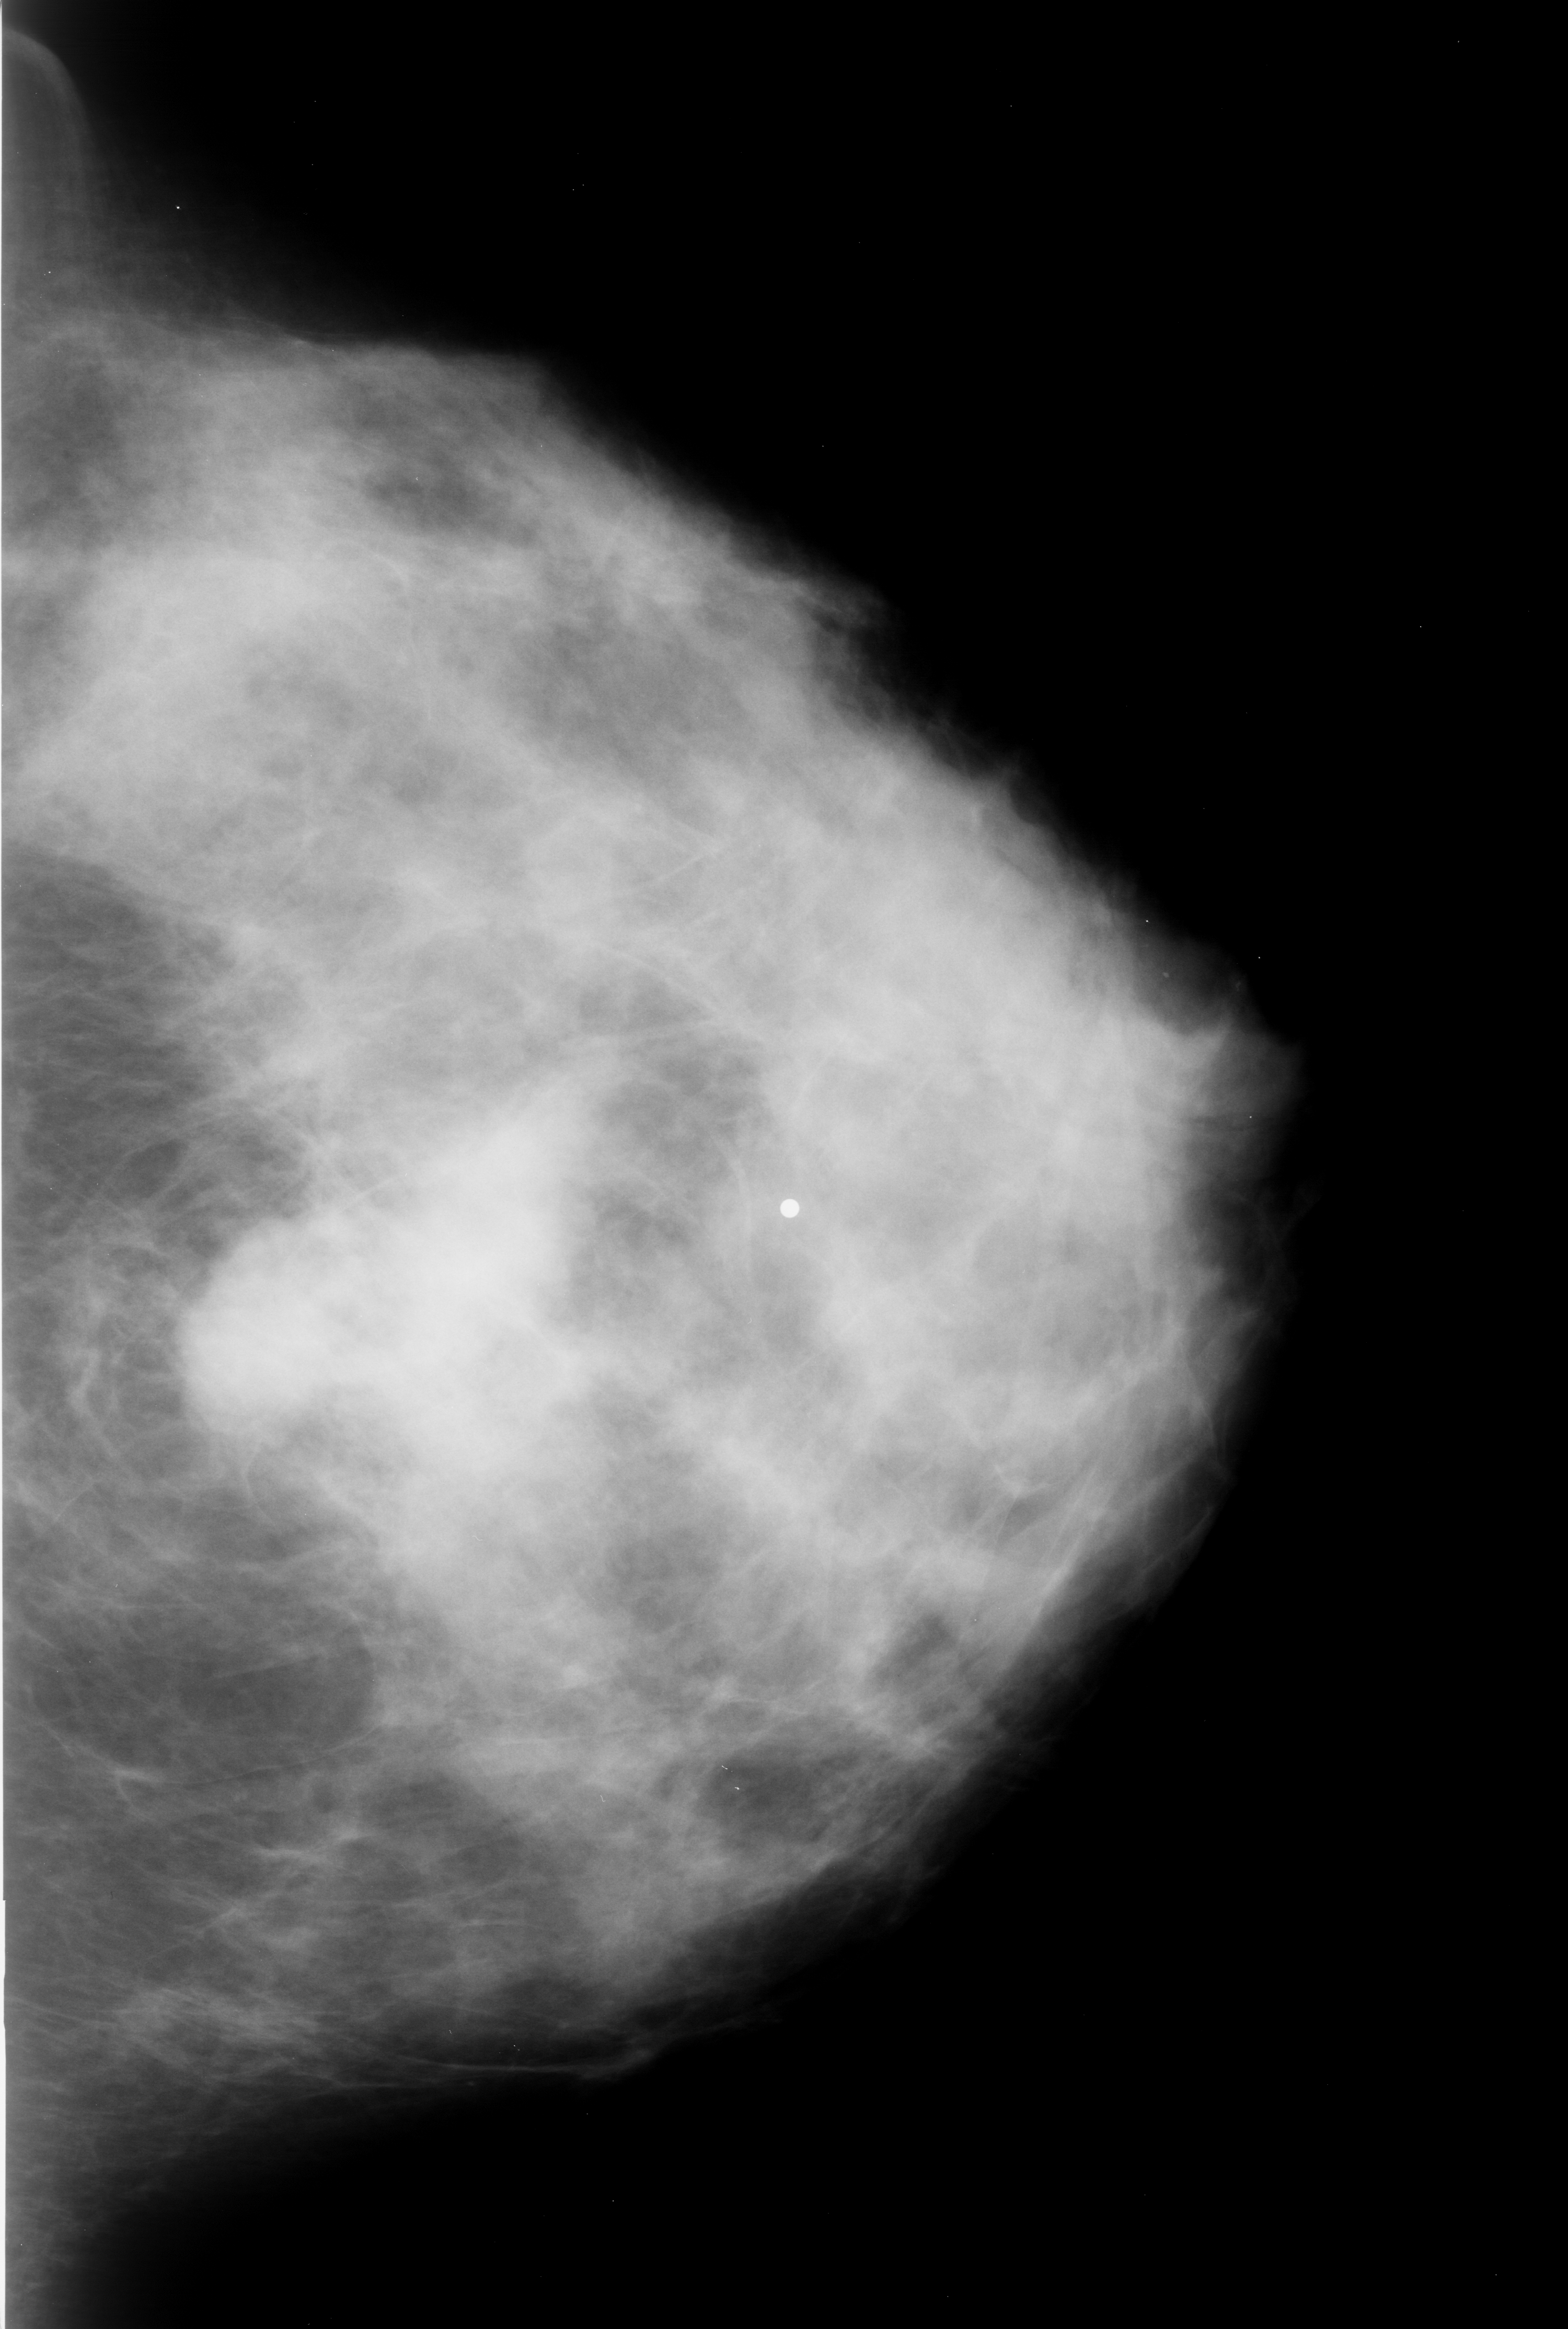
Mammogram (digitized film); left breast; CC view; breast composition: heterogeneously dense (BI-RADS density category 3 of 4).
Abnormality record for this image: mass, shape lobulated / irregular, margins obscured / ill defined; BI-RADS assessment category 4; pathology result (as recorded, not read from the image): malignant.